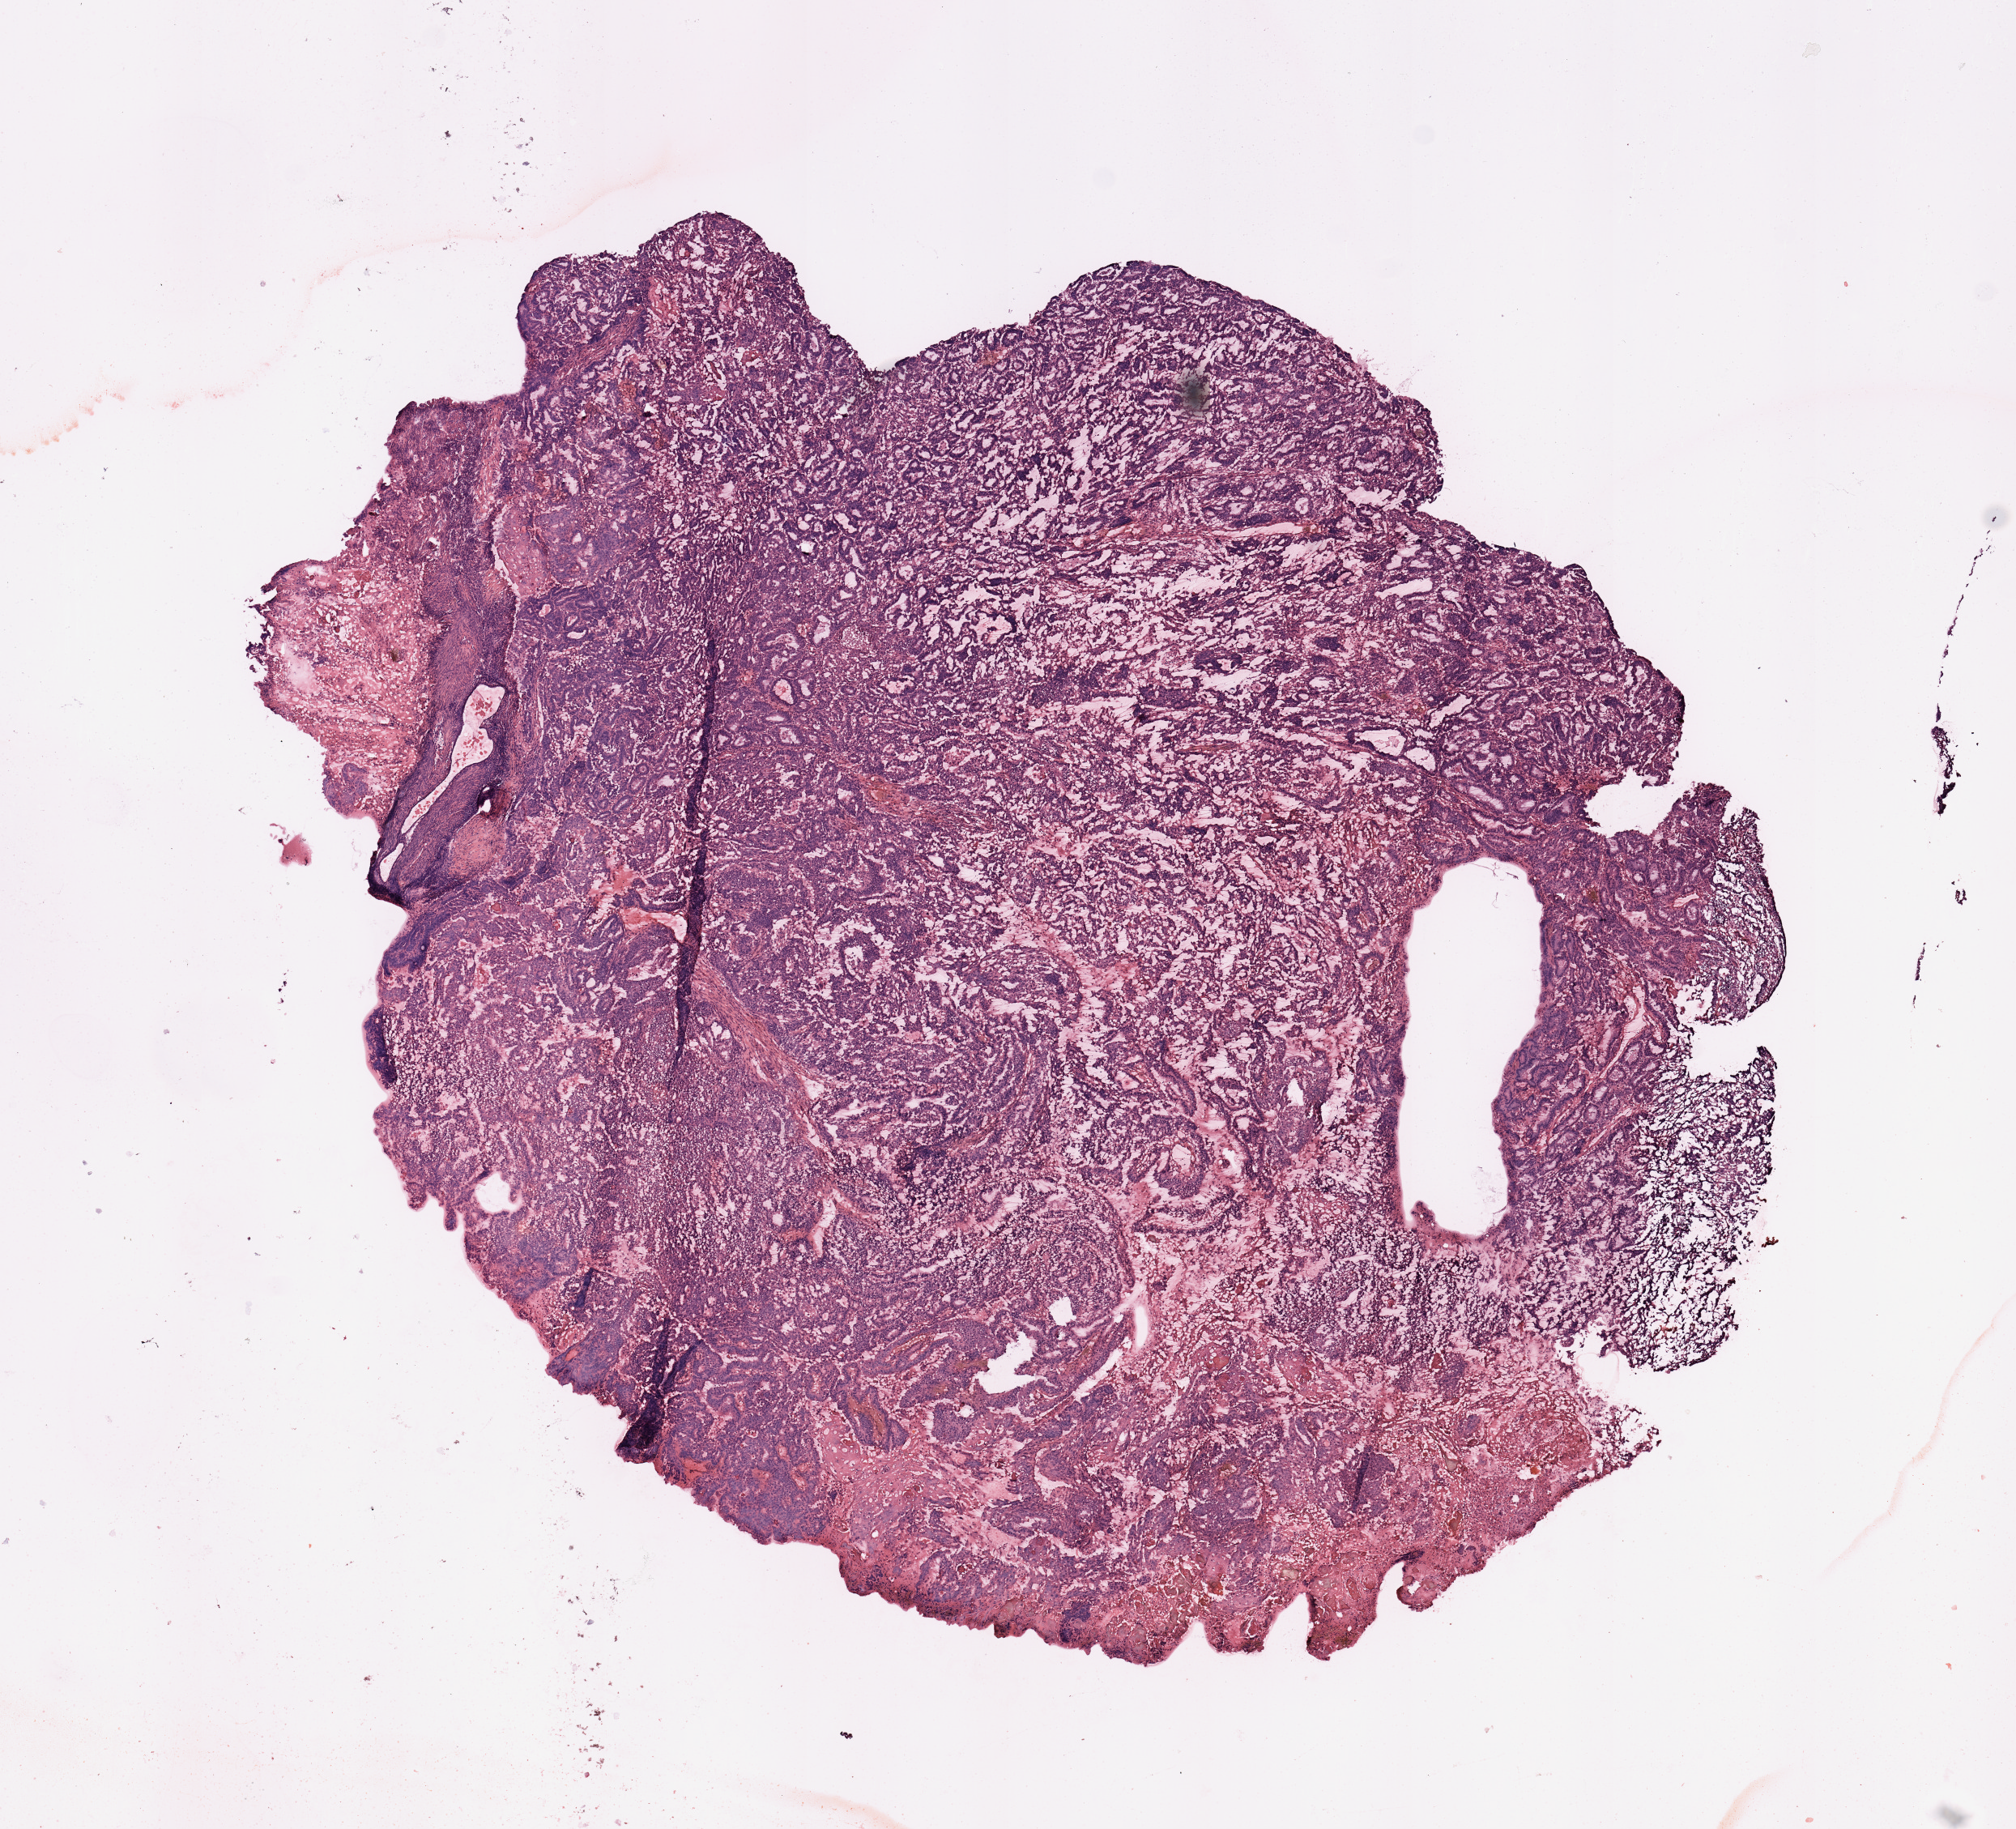
Whole-slide histology image, H&E-stained — shown as a low-resolution overview of the whole scanned area (about 9.8 x 8.9 mm, slide scanned at 20x). Tumour tissue sample, sampled site: uterus. Female, 65 y/o. Histologic grade: G2 (moderately differentiated). Composition of this section per pathologist review: tumour nuclei 90%, necrosis 0%.
AJCC pathologic stage: I. Histologic diagnosis: Endometrioid adenocarcinoma, NOS.